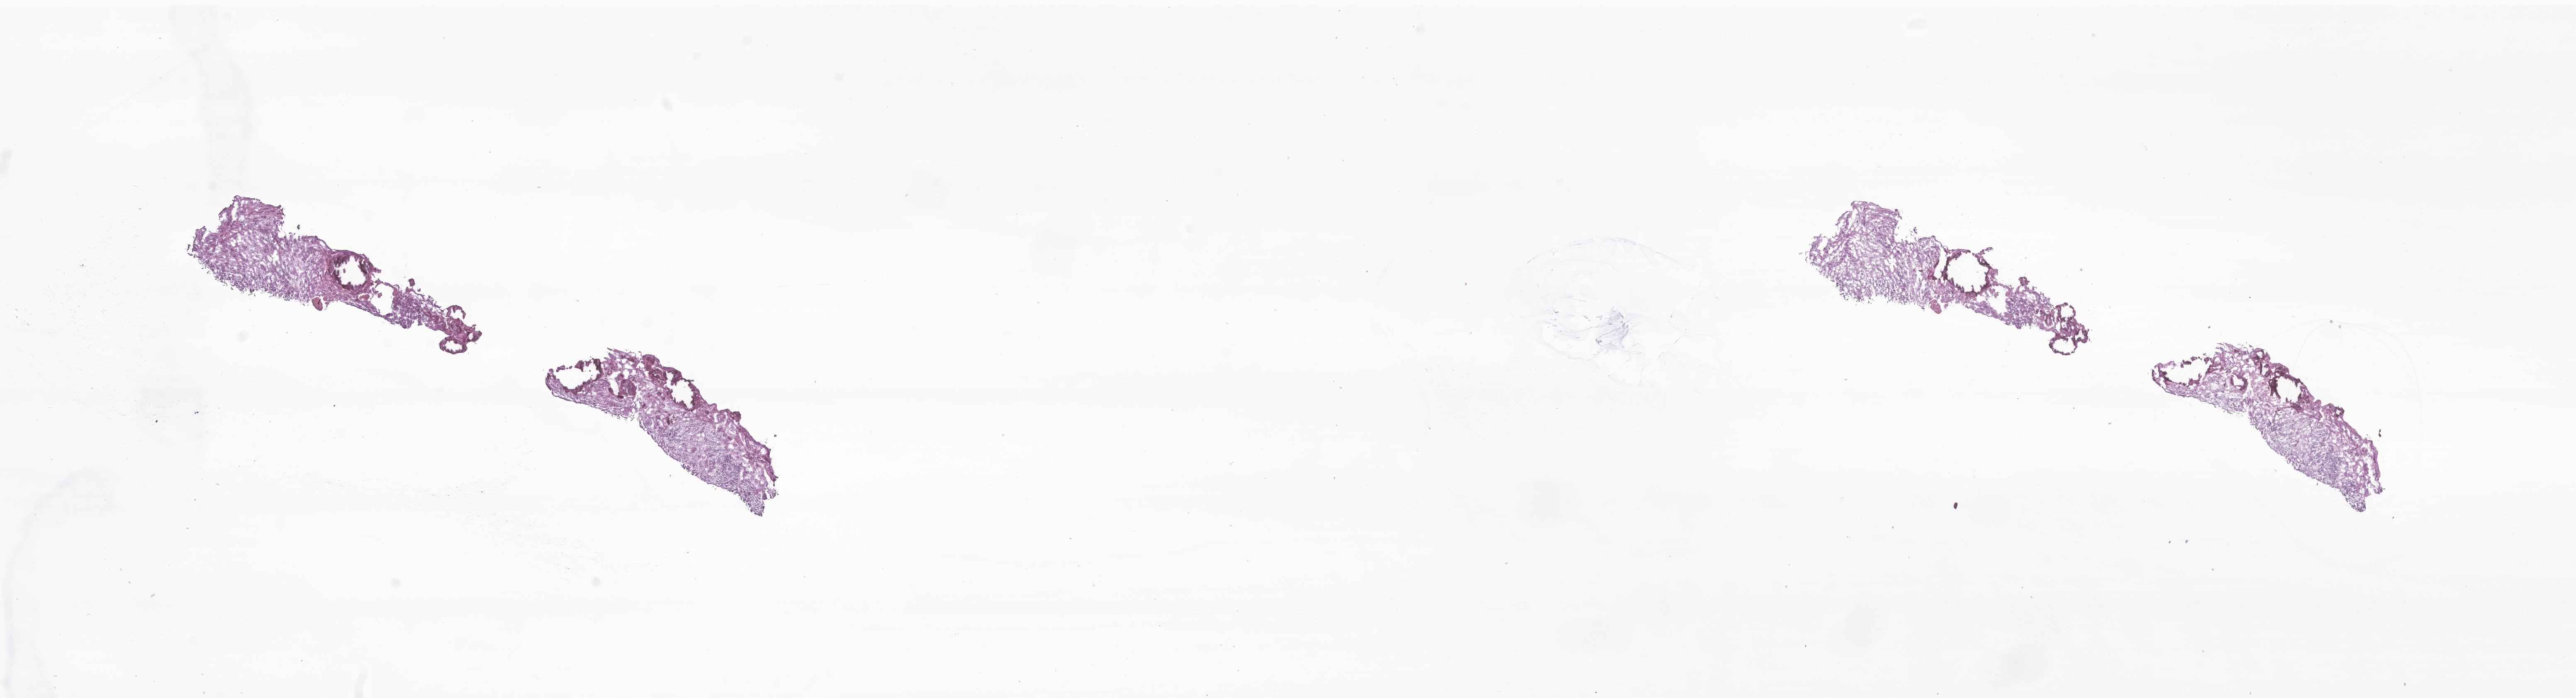
Digitized H&E-stained section of tumor tissue from the abdomen, shown as a low-resolution overview of the whole scanned area (about 26.2 x 7.1 mm). Frozen section. Patient: male, age 726 days (about 2.0 years).
* recorded diagnosis: Neuroblastoma, NOS